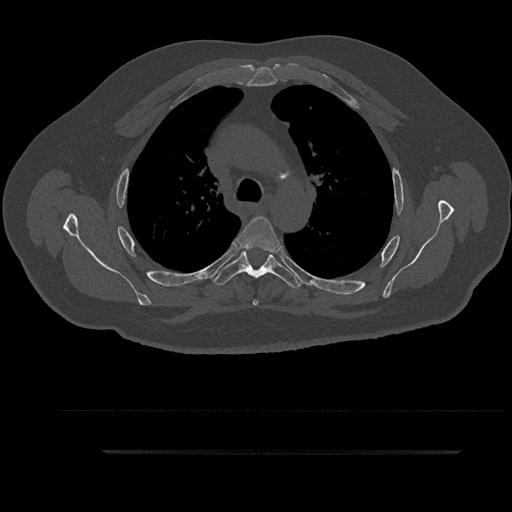
CT including the spine, one axial slice. Position 648 of 797 along the scan axis. Bone window (W 1800 / L 400 HU). 512 × 512 image matrix. Patient: male, 63 years. From the clinical record (not read from this slice): primary cancer: renal; vertebrae with lytic lesions (as recorded): T8.
Annotated regions visible in this slice (semi-automatically segmented with operator editing):
- T3 vertebra: bounding box (x1, y1, x2, y2) in pixels: (267, 258, 269, 260)
- T4 vertebra: (236, 216, 281, 306)
- T5 vertebra: (214, 247, 300, 290)